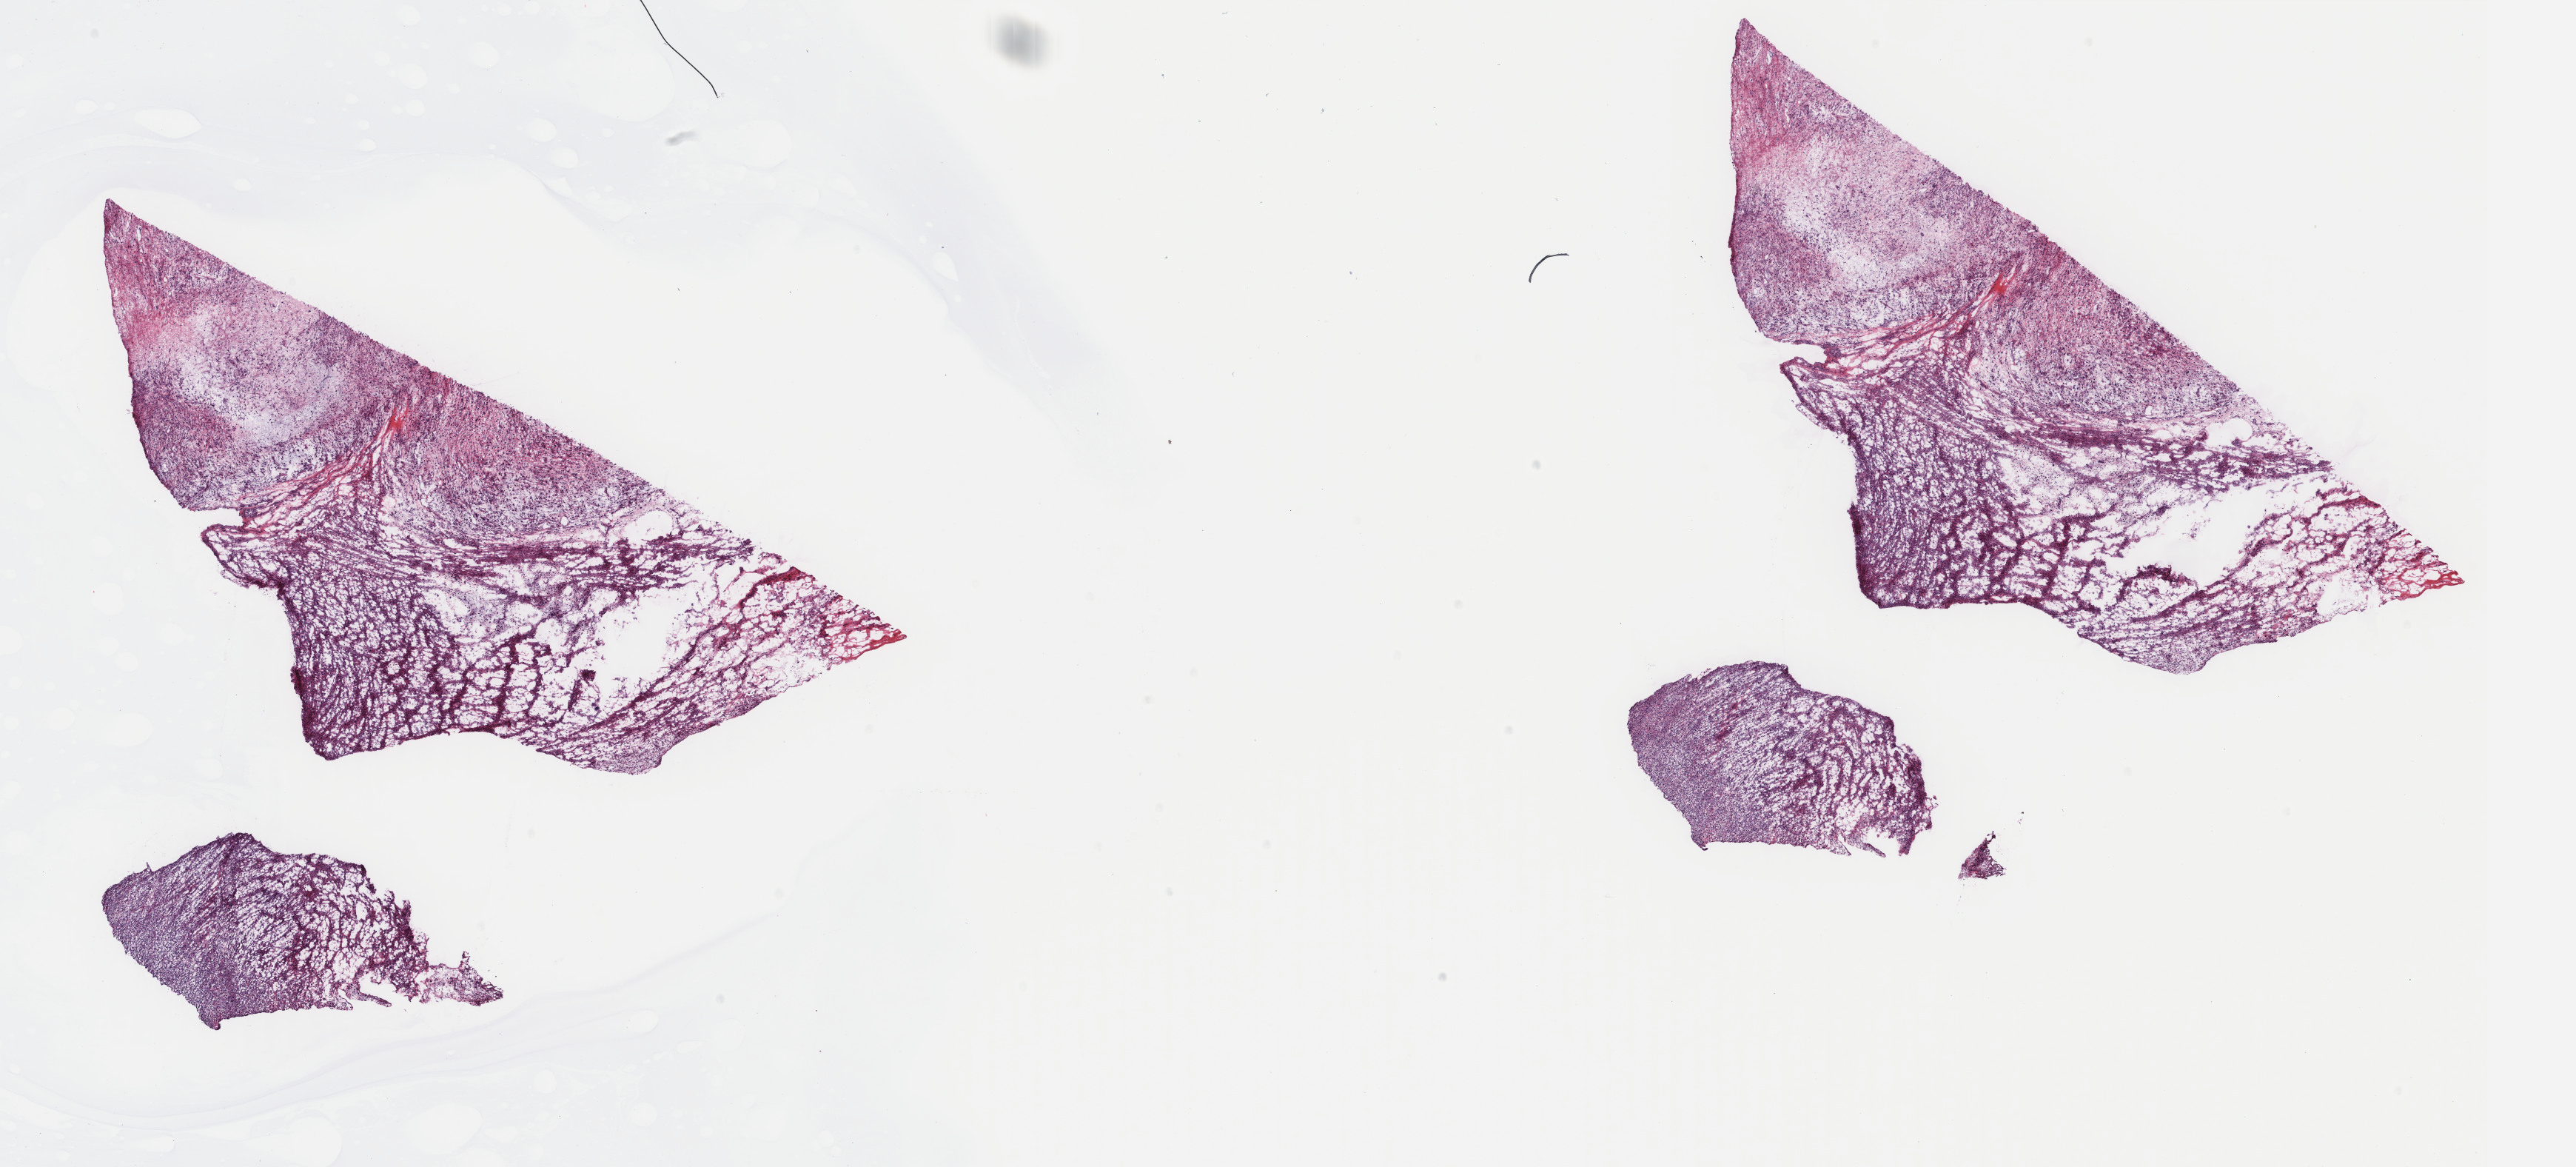
H&E-stained whole-slide image, a low-resolution overview of the entire scanned area, about 27.6 x 12.5 mm. Frozen section from the top of the tissue portion. Connective, subcutaneous and other soft tissues, primary tumour sample. Female patient; age at initial diagnosis 66 years.
Pathologic diagnosis: Fibromyxosarcoma (connective, subcutaneous and other soft tissues of lower limb and hip).